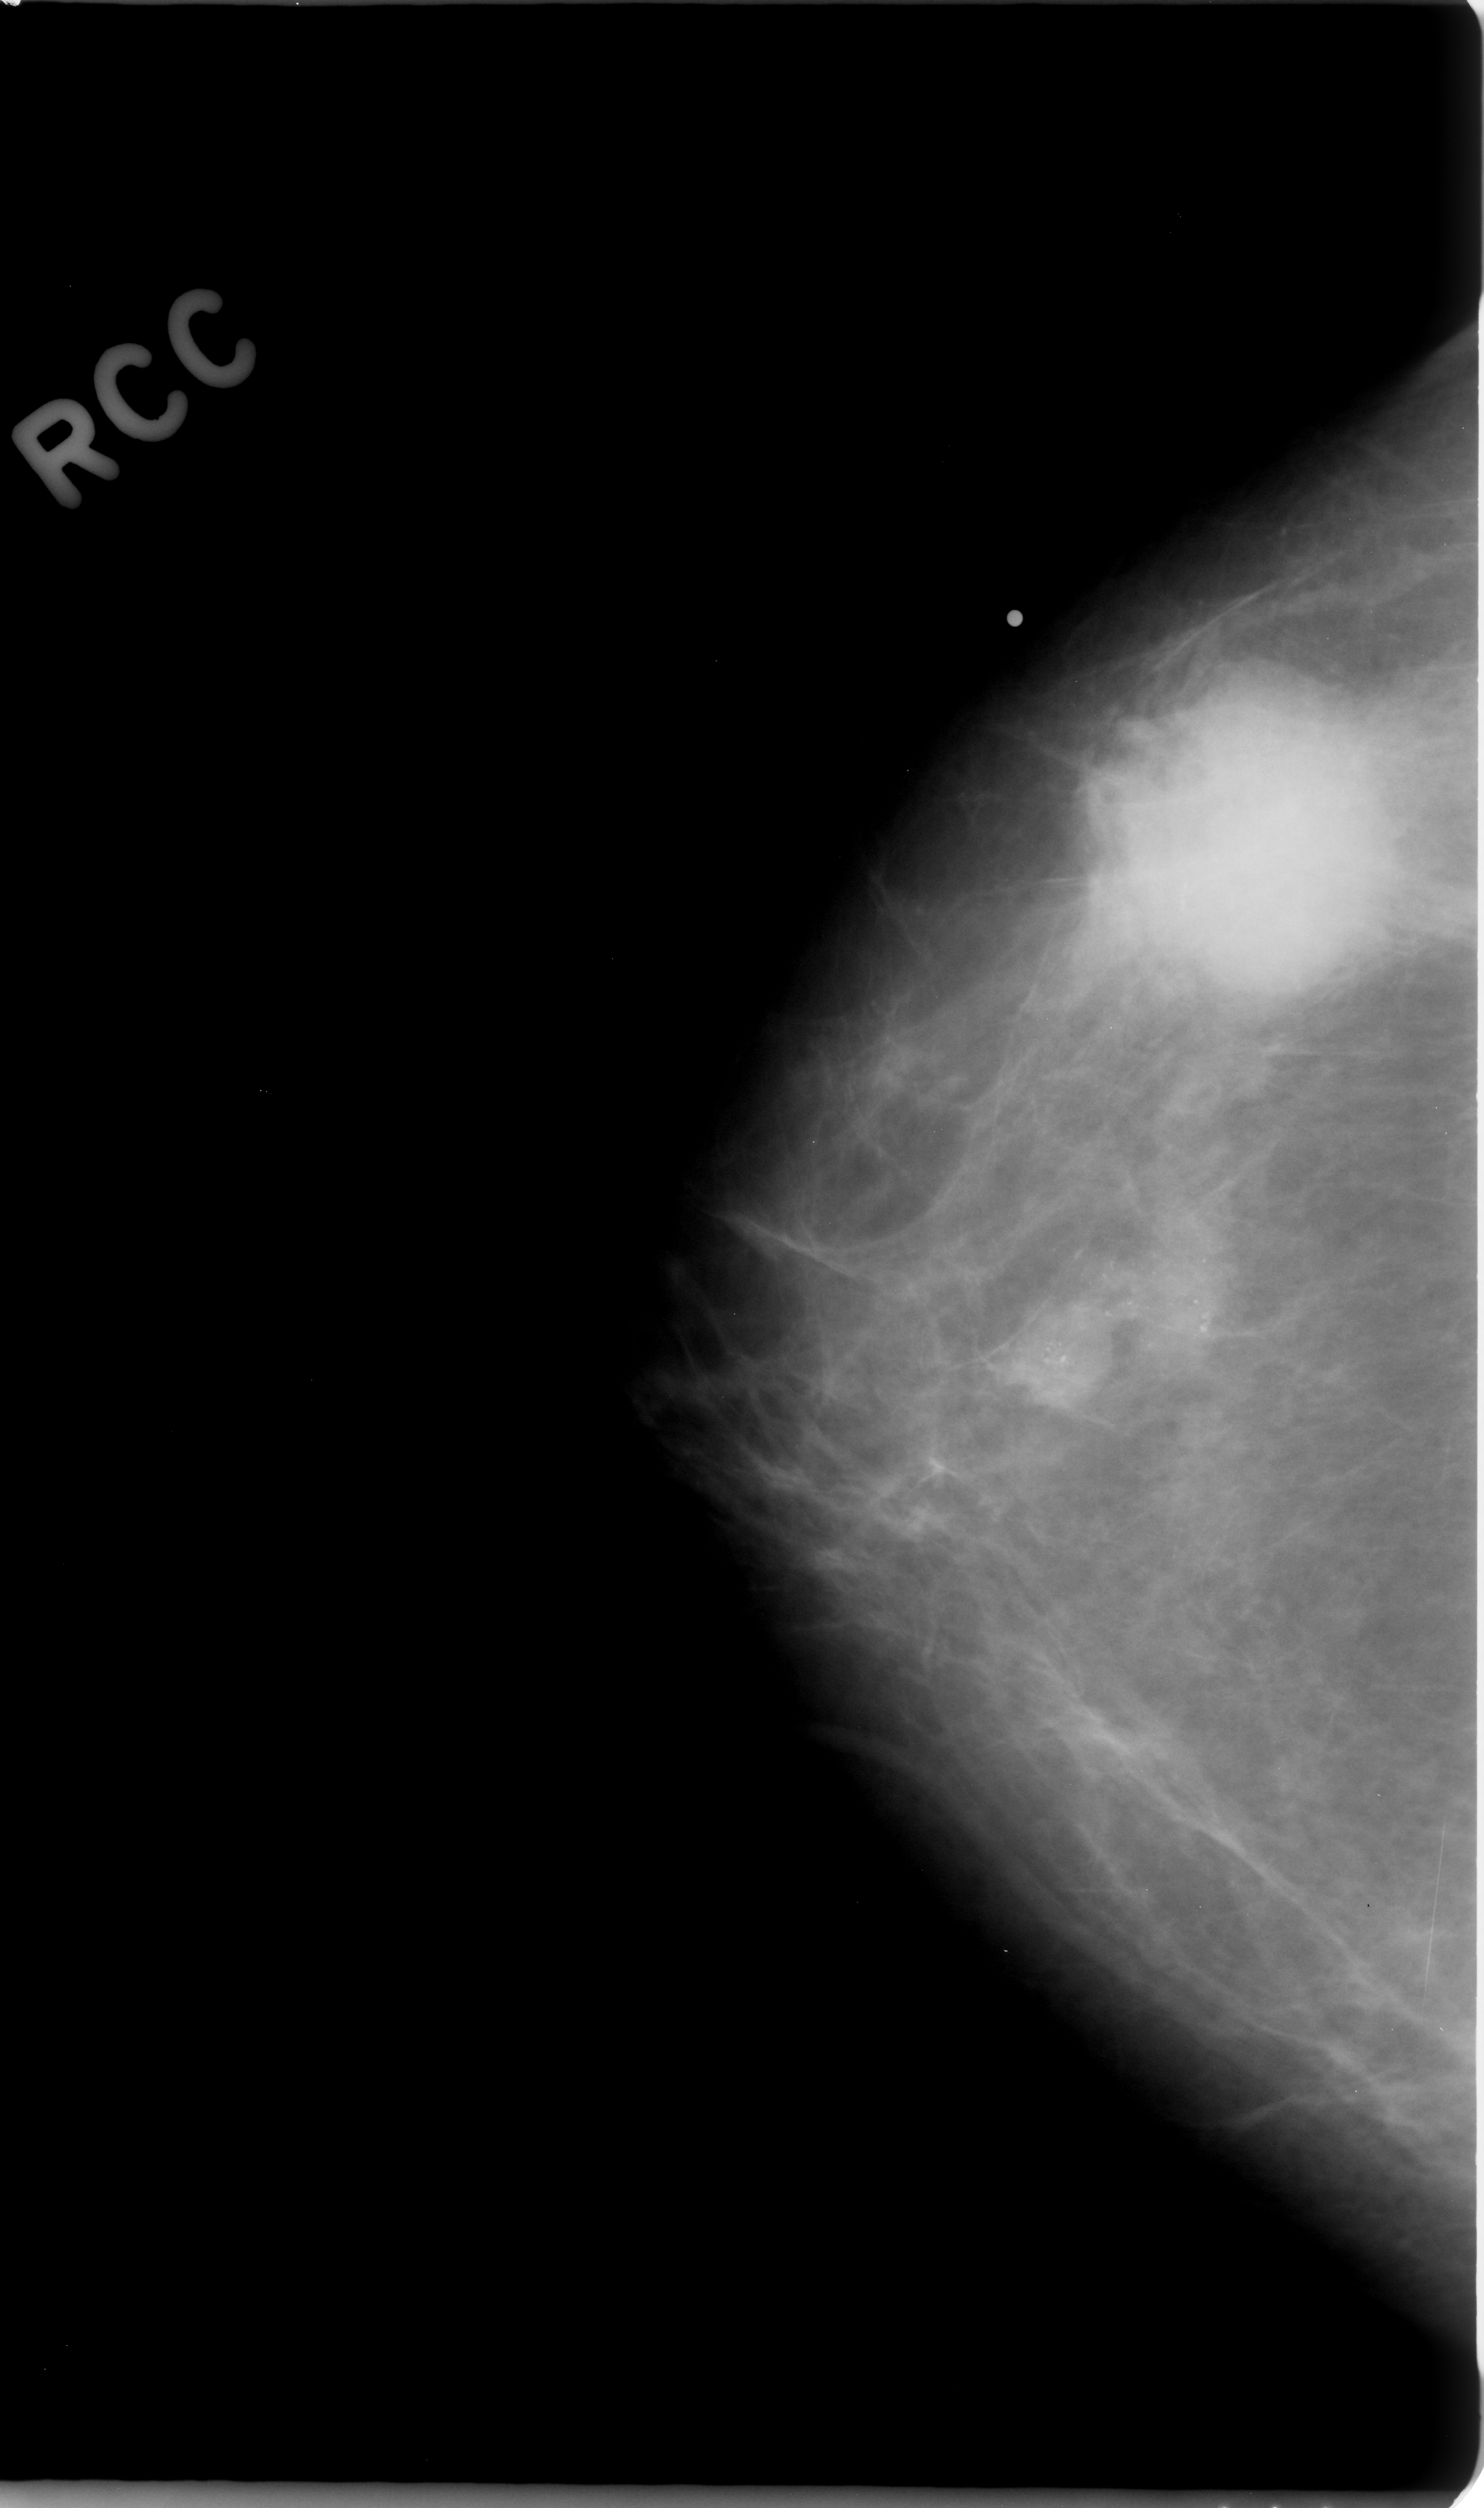
Mammogram (digitized film); right breast; CC view; breast composition: almost entirely fatty (BI-RADS density category 1 of 4); 1484 × 2508 image matrix.
Expert-marked regions of interest on this film, with their recorded descriptors:
- calcifications, morphology amorphous, distribution clustered; BI-RADS assessment category 5; pathology result (as recorded, not read from the image): malignant: bounding box (x1, y1, x2, y2) in pixels: (933, 537, 1481, 1485)